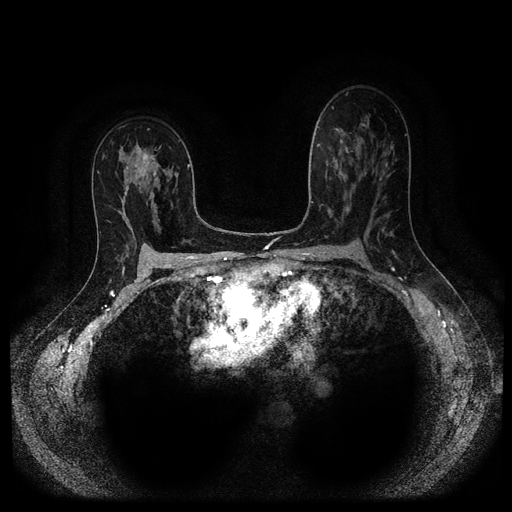
Breast MRI (dynamic contrast-enhanced, multi-phase), one axial slice; slice 60 of 116 in the series (ordered by position); dynamic contrast-enhanced series, time point 2 of 5 at this slice position (early post-contrast); 1.5 T; TE 2.6 ms, TR 5.3 ms; 2.2 mm slice thickness; 512 × 512 image matrix, field of view 340 × 340 mm. Patient: female, 50 years.
Annotated regions visible in this slice (semi-automatic segmentation, software-assisted and operator-edited):
- breast lesion (labelled 'tumour' in the annotation; benign lesions carry a separate 'benign' label): bounding box (x1, y1, x2, y2) in pixels: (130, 143, 163, 183)